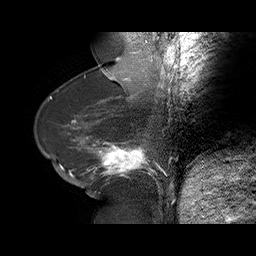
Breast MRI (dynamic contrast-enhanced), one sagittal slice; slice 26 of 75 in the series (ordered by position); dynamic contrast-enhanced series, time point 2 of 6 at this slice position (early post-contrast); 1.5 T; TE 4.5 ms, TR 32.4 ms; 3 mm slice thickness; 256 × 256 image matrix. Female patient. From the clinical record (not read from this slice): setting: breast cancer imaged before/during neoadjuvant chemotherapy; receptor status: HR-positive, HER2-negative.
Structures marked on this image (semi-automatically segmented with operator editing):
- analysis volume of interest (the breast-tissue region the enhancement analysis was run in; not a lesion): box from (x=58, y=134) to (x=166, y=191) px
- tumour enhancement mask (voxels above the 100 % enhancement threshold inside the analysis volume of interest): (x=60, y=136)–(x=165, y=178)